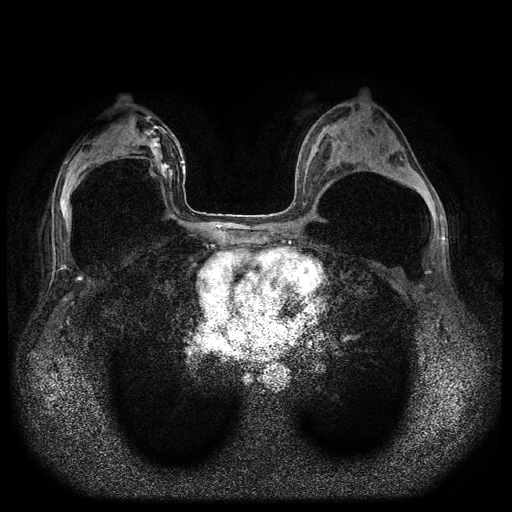
Breast MRI (dynamic contrast-enhanced, multi-phase), one axial slice. Position 47 of 116 along the scan axis. Dynamic contrast-enhanced series, time point 2 of 5 at this slice position (early post-contrast). 1.5 T. TE 2.6 ms, TR 5.4 ms. 2 mm slice thickness. 512 × 512 image matrix, field of view 340 × 340 mm. Female patient, age 42 years.
Annotated regions visible in this slice (semi-automatic segmentation, software-assisted and operator-edited):
- breast lesion (labelled 'tumour' in the annotation; benign lesions carry a separate 'benign' label): bounding box (x1, y1, x2, y2) in pixels: (144, 129, 173, 189)